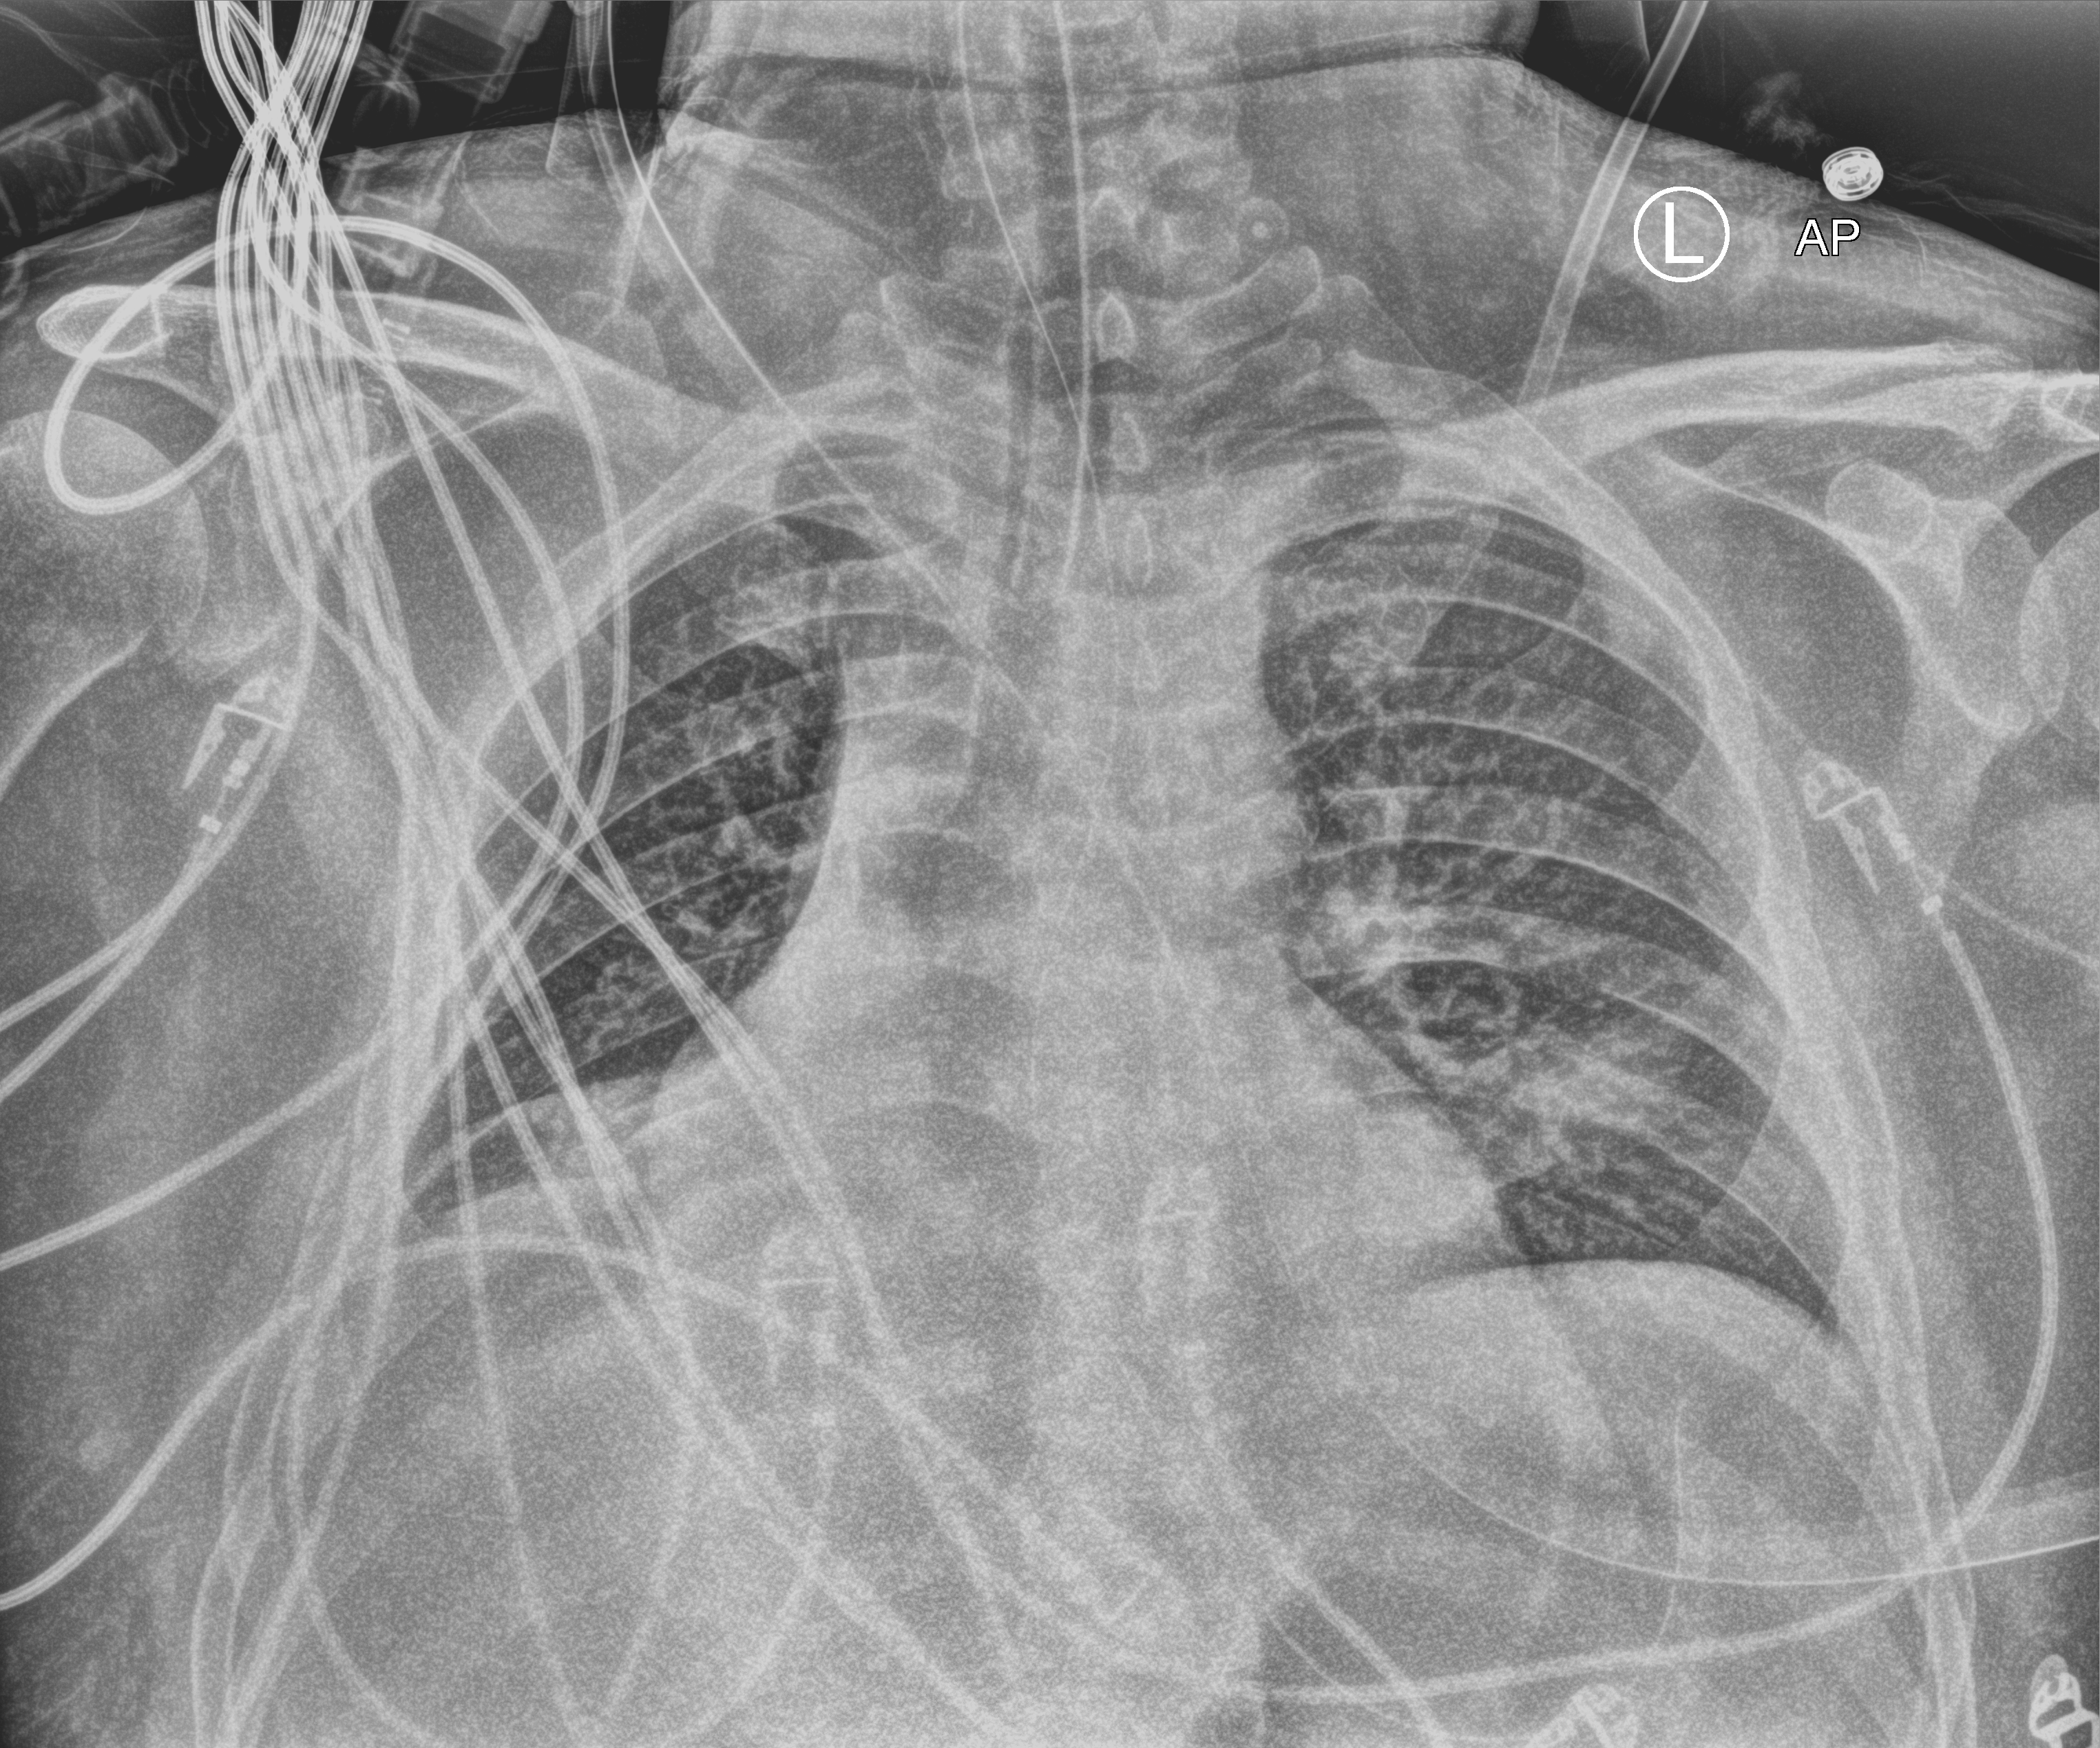
Portable chest radiograph; anteroposterior (AP) projection. Male patient hospitalised with COVID-19, age 18–59 years.
Admission-level facts for this patient (not findings on this image; timing relative to this image not recorded): admitted to intensive care during this hospital stay: yes; mechanically ventilated during this hospital stay: yes.